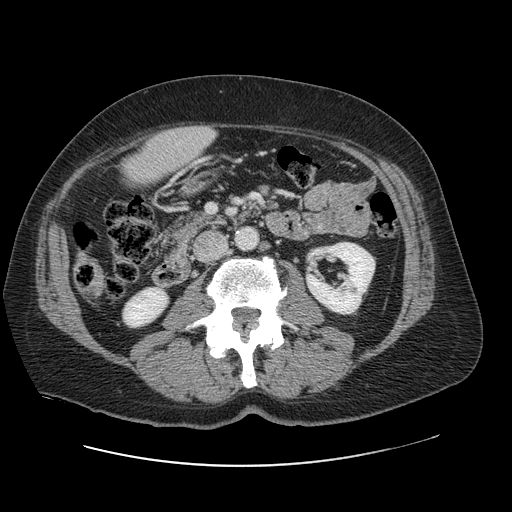
Contrast-enhanced abdominal CT, one axial slice; position 18 of 138 along the scan axis; 120 kVp; intravenous contrast given; soft-tissue window (W 400 / L 40 HU); 2.5 mm slice thickness; 512 × 512 image matrix, field of view 402 × 402 mm. Male patient, age 71 years. Case-level facts recorded for this patient, not image findings: diagnosis: colorectal cancer liver metastases, imaged before liver resection; multiple liver metastases: no; largest metastasis: 3.3 cm; disease in both lobes: no.
Outlined on this slice (expert manual segmentation):
- liver: bounding box <123,127,215,184> (left, top, right, bottom; pixels)
- planned liver remnant (the part of the liver to remain after resection): <123,139,172,185>